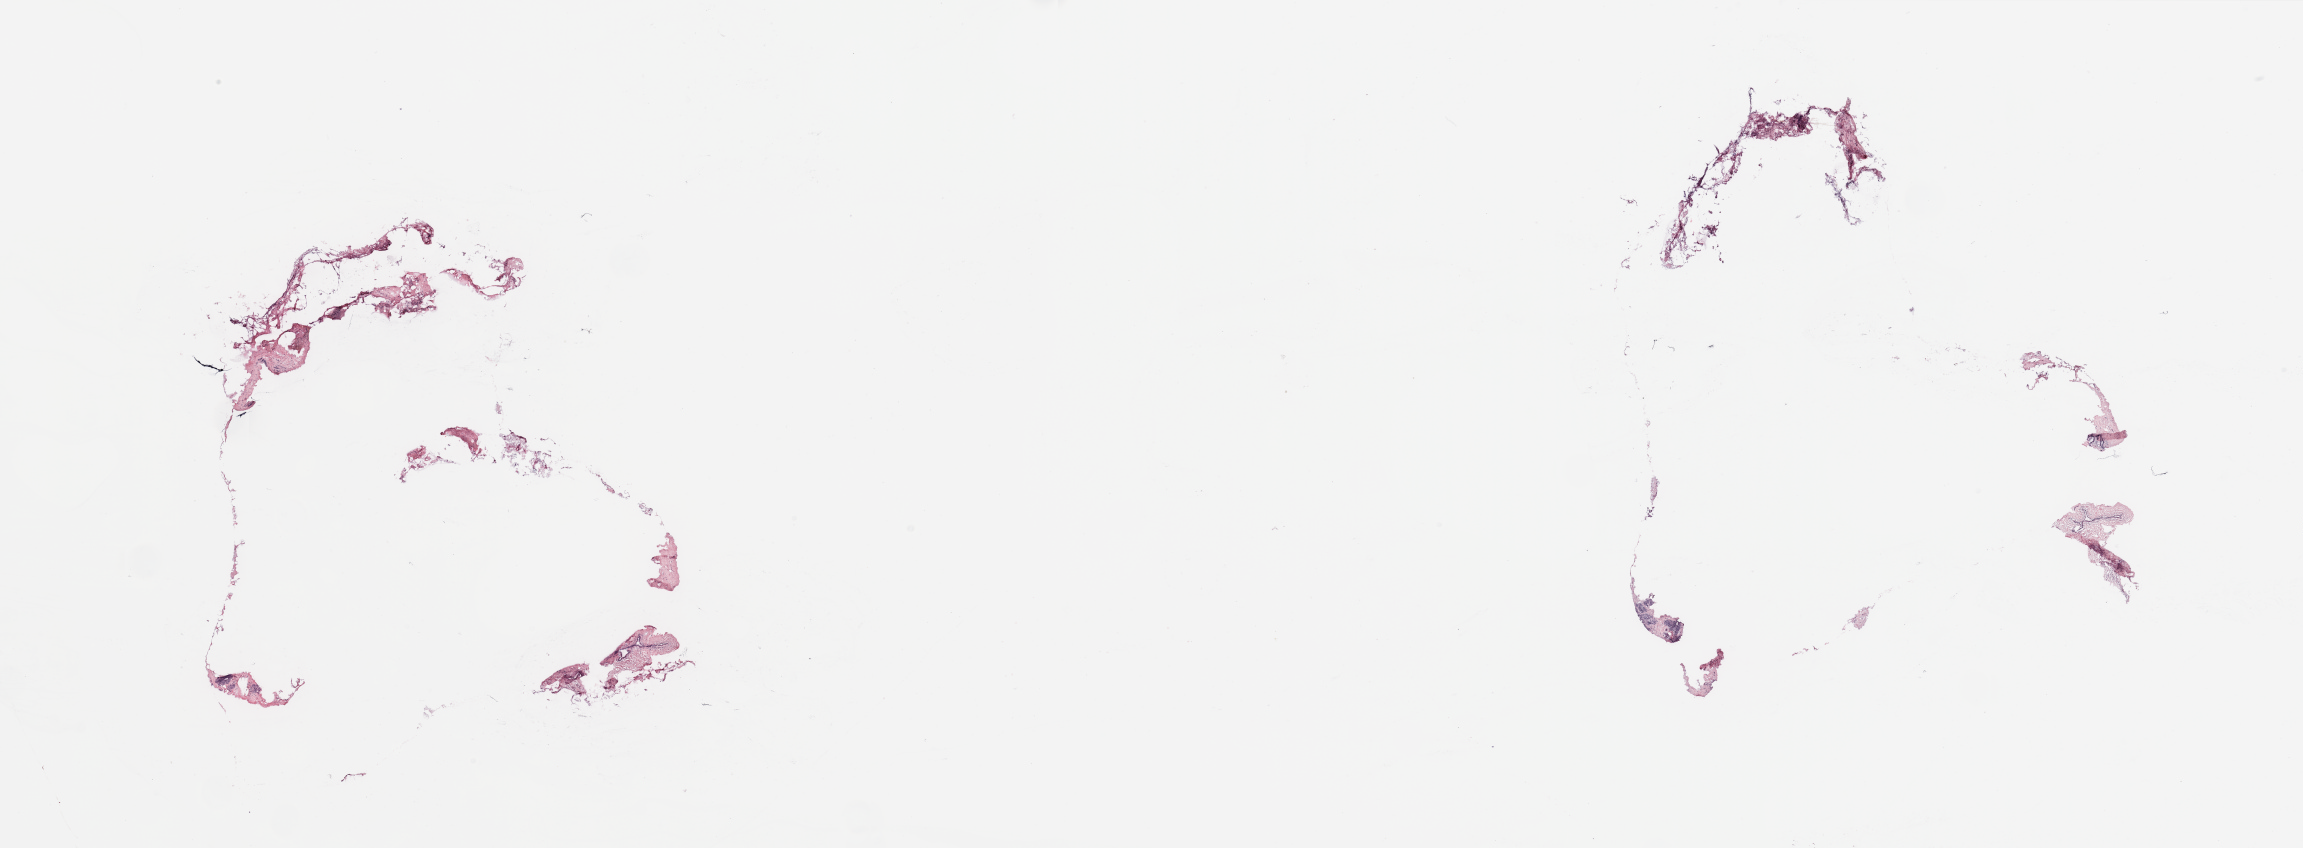
Digitized H&E-stained tissue section (whole slide) — whole scanned area (about 36.4 x 13.4 mm, slide scanned at 20x) shown as a low-resolution overview; breast, tissue type not recorded.
Patient diagnosis (cohort enrolment): breast cancer (breast).